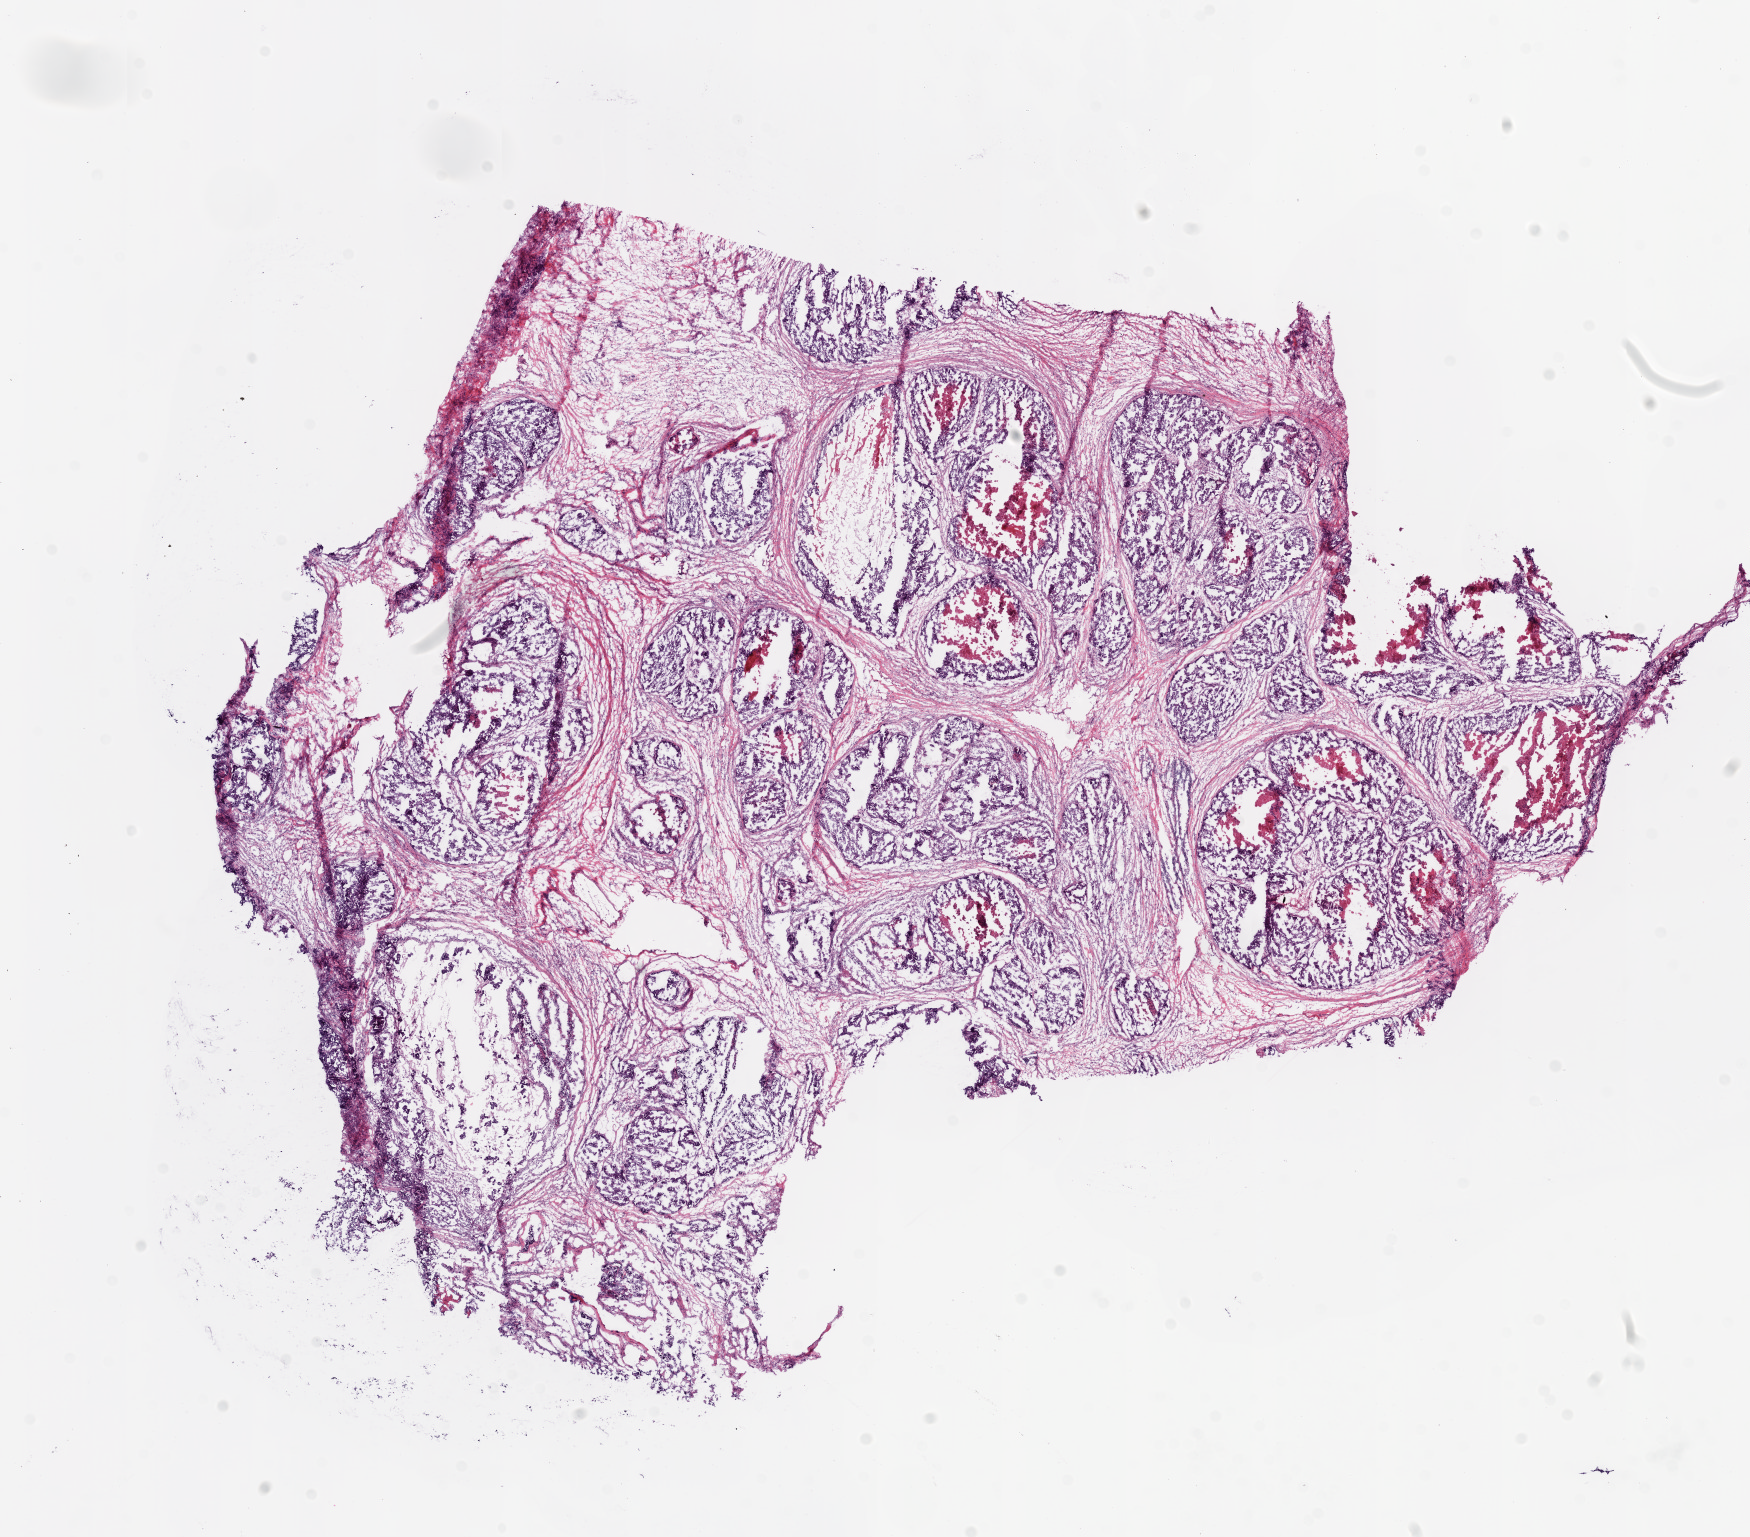
Digitized Hematoxylin and eosin (H&E) stained tissue section (whole slide), a low-resolution overview of the entire scanned area, about 14.0 x 12.3 mm (acquisition: 20x scan). Frozen section from the bottom of the tissue portion. Sample: primary tumour, ovary. Female, age 74 years at initial diagnosis. Histologic grade: G3 (poorly differentiated). Pathologist review of this section (percent, as recorded): tumour cells 80%, tumour nuclei 90%, normal cells 0%, stromal cells 10%, necrosis 10%.
- diagnosis: Serous cystadenocarcinoma, NOS
- laterality: bilateral
- FIGO stage: IIIB